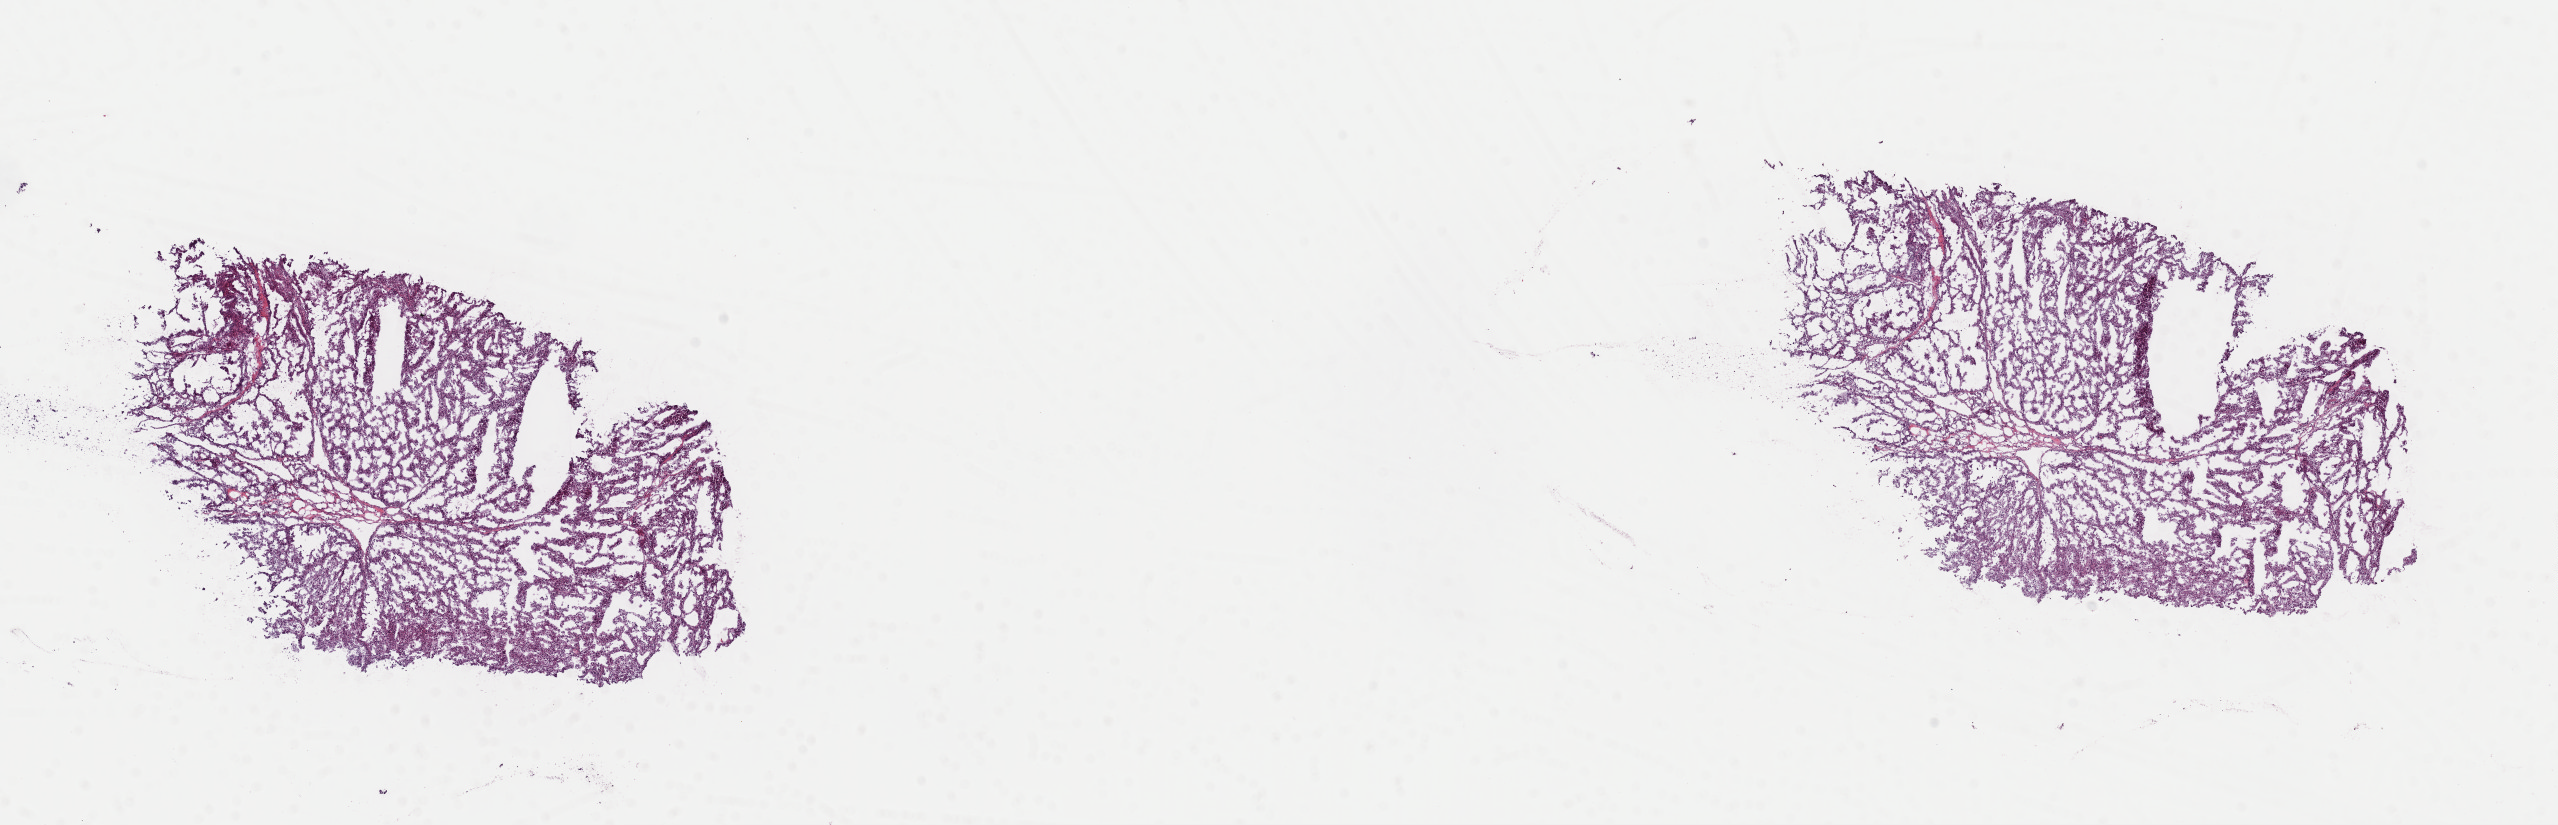
Whole-slide histology image, H&E — low-resolution overview of the scanned area, about 20.2 x 6.5 mm (acquisition: 40x scan), frozen section from the top of the tissue portion, kidney, primary tumour sample. Female, age 54 years at initial diagnosis. Histologic grade: G4 (undifferentiated). Slide review estimates, as recorded: tumour cells 100%, tumour nuclei 80%, normal cells 0%, stromal cells 0%, necrosis 0%. Inflammatory infiltration, as recorded: lymphocyte infiltration 2%, monocyte infiltration 0%, neutrophil infiltration 0%.
* lymph nodes positive (case pathology): 0 of 1 examined
* AJCC pathologic stage: IV (7th edition)
* diagnosis: Clear cell adenocarcinoma, NOS
* TNM: T1b N0 M1